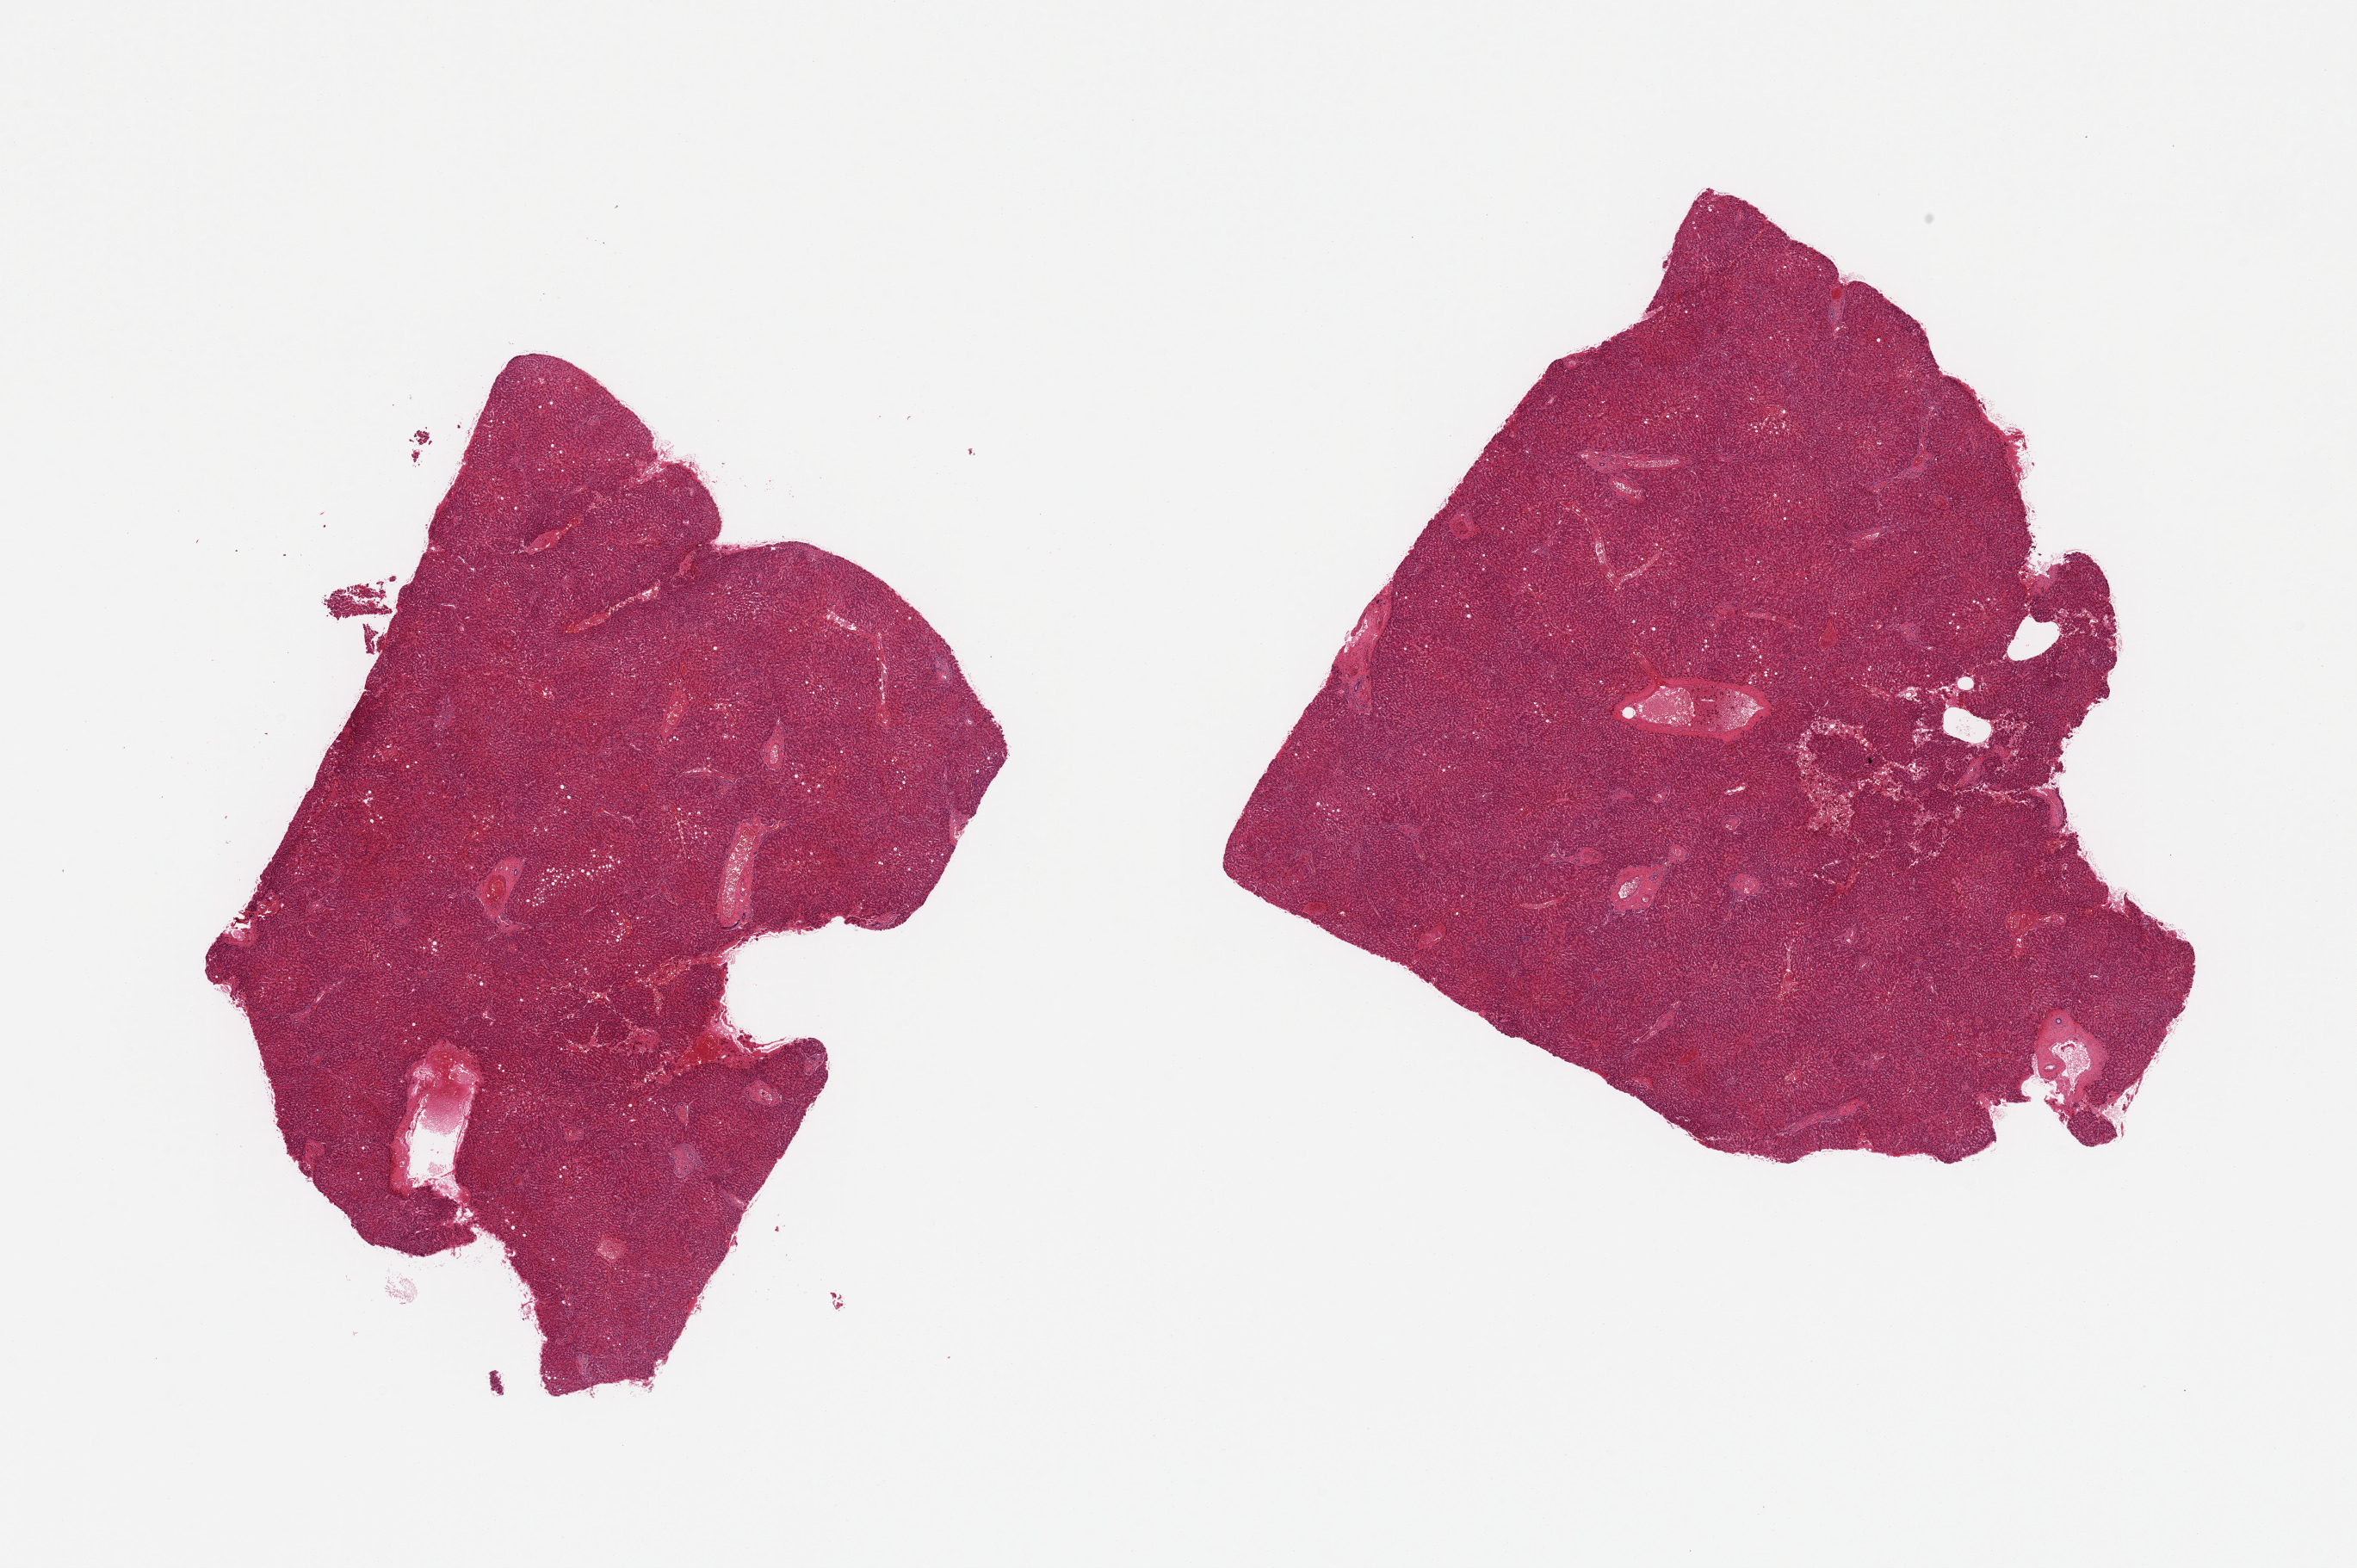
Digitized haematoxylin and eosin-stained section — whole scanned area (about 21.7 x 14.4 mm) shown as a low-resolution overview; PAXgene-fixed paraffin-embedded (PFPE) section; target tissue: liver; donor tissue sample. Donor sex: male.
Review note (as recorded): 2 pieces; <5% macrovesicular steatosis; focal hemorrhages.